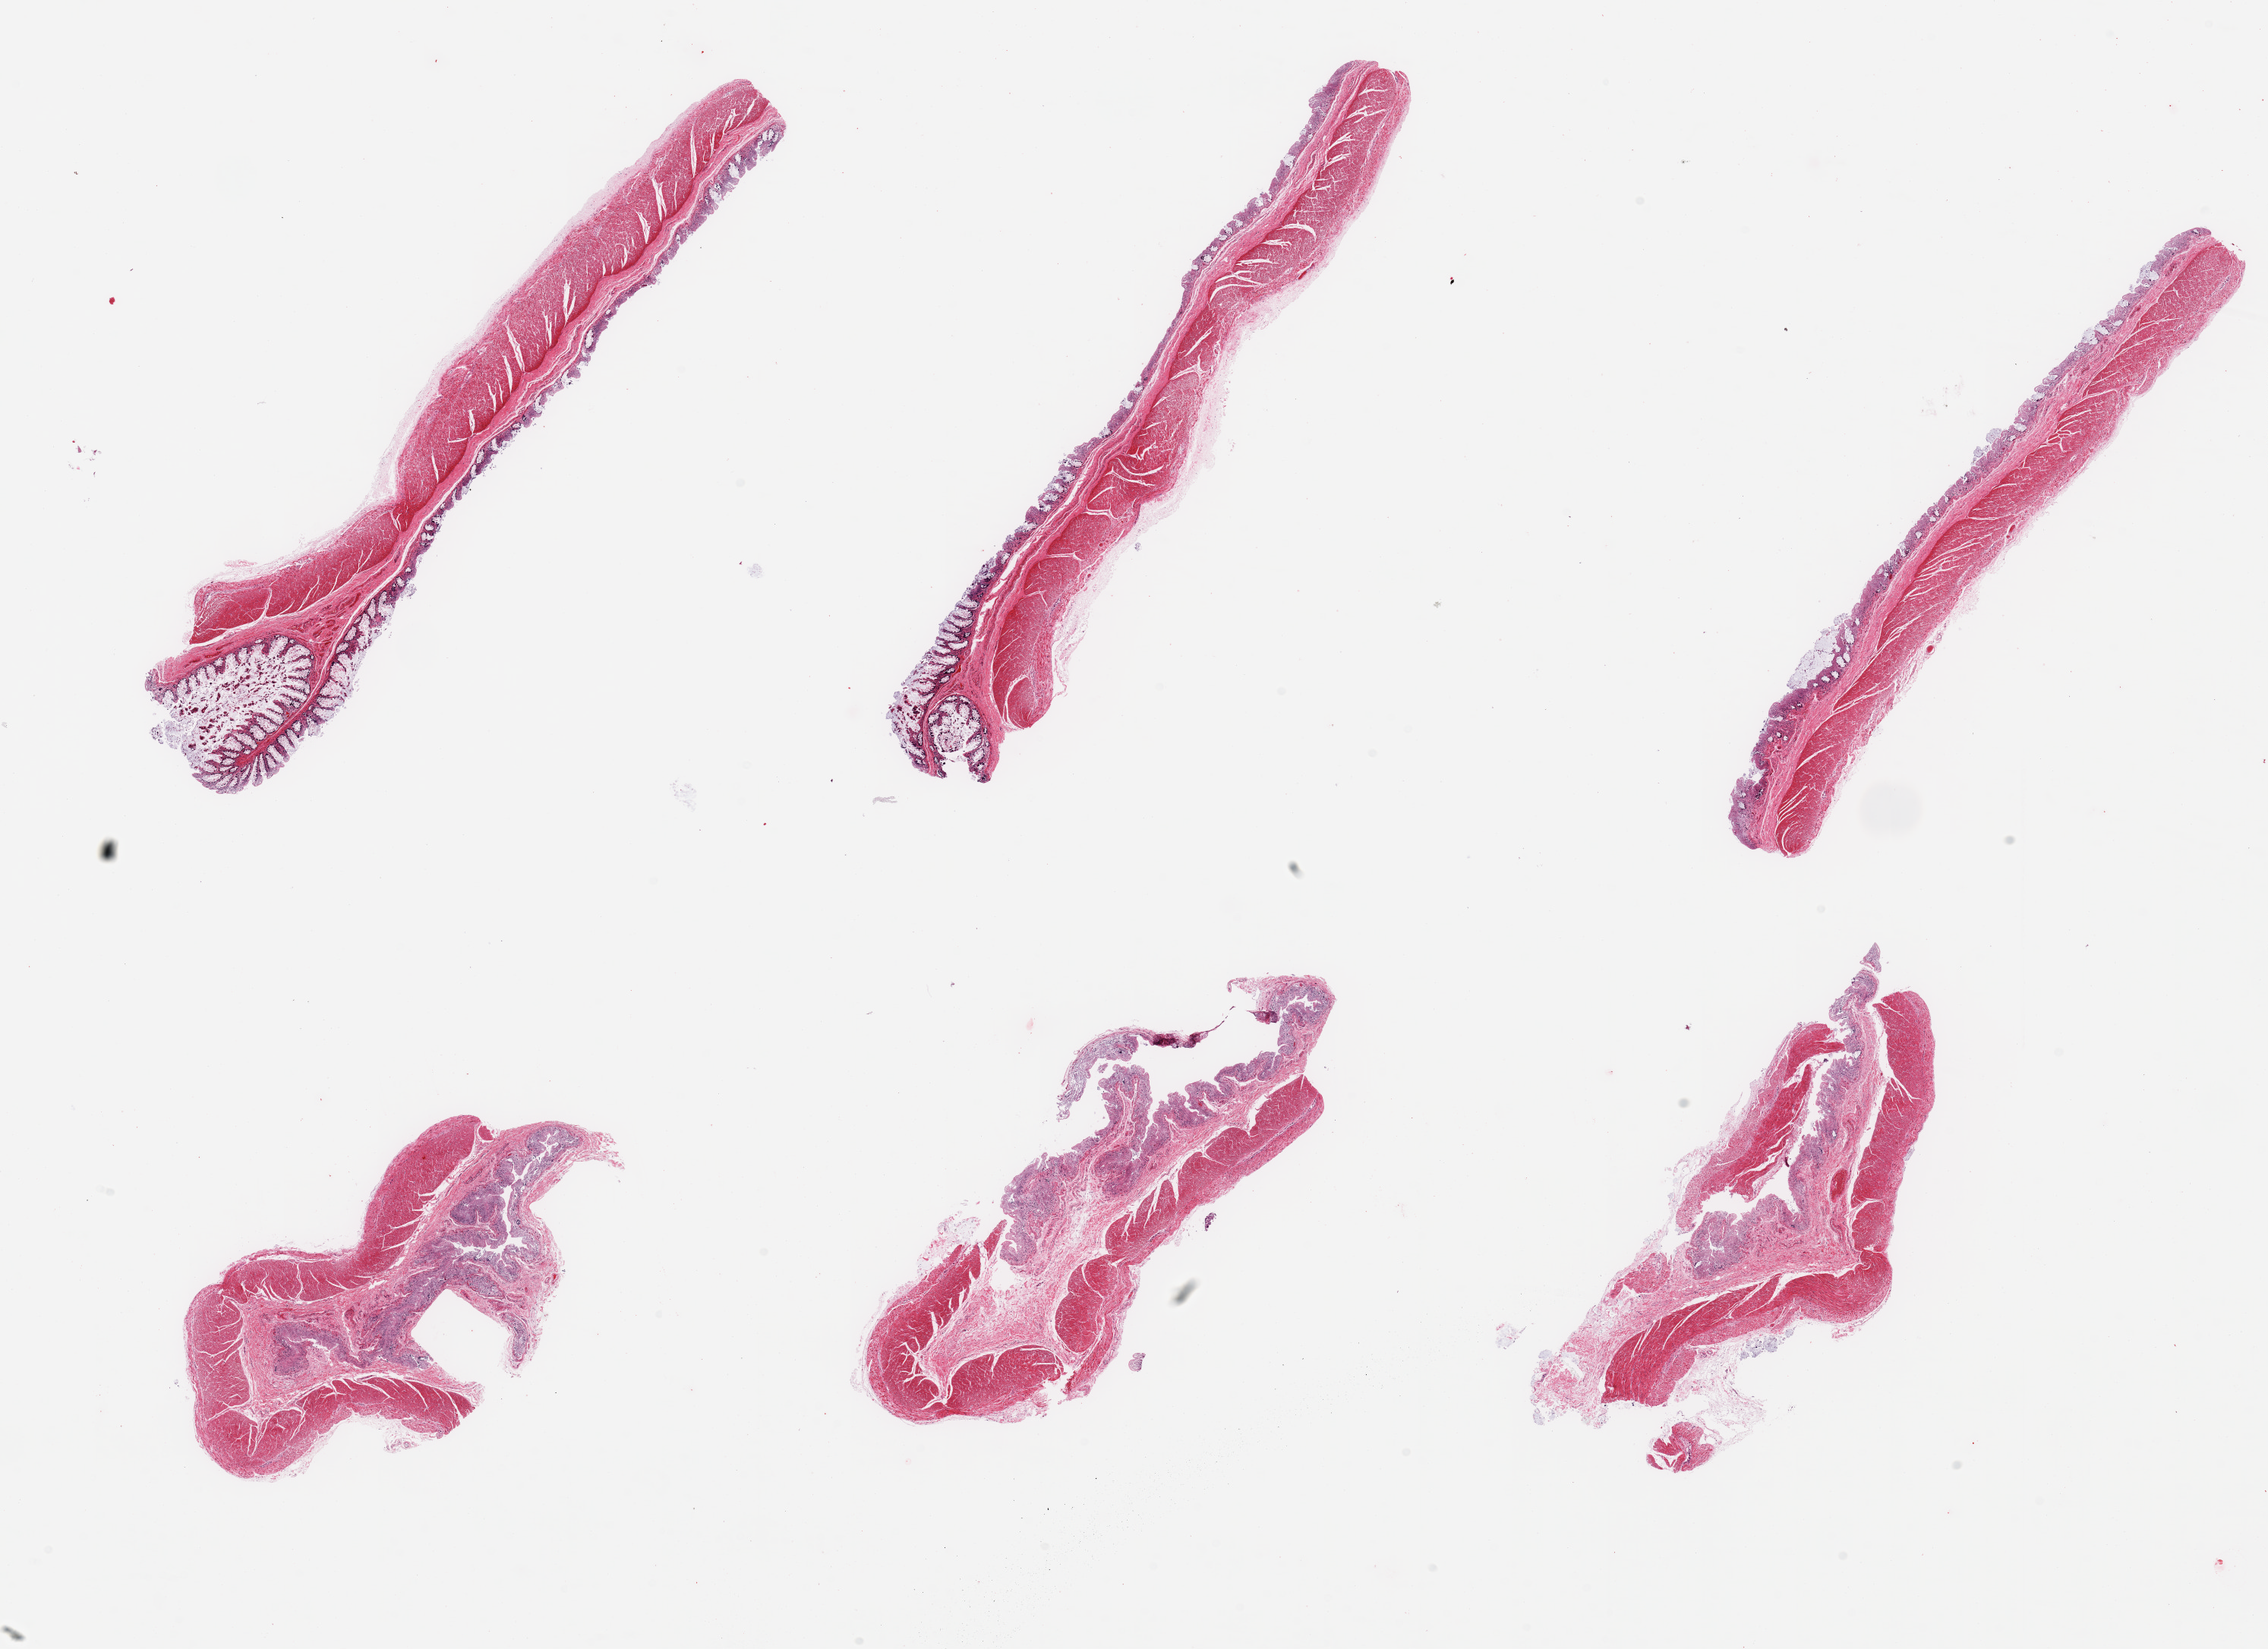
Digitized haematoxylin and eosin-stained section, brightfield — low-resolution overview of the scanned area, about 23.6 x 17.2 mm (from a 20x scan); PAXgene-fixed, paraffin-embedded tissue; sampled site (target tissue): transverse colon; tissue donor sample.
Review note (as recorded): 6 pieces; 3 have mucosa moderately autolyzed; 3 have mucosa totally autolyzed; muscularis intact in all.